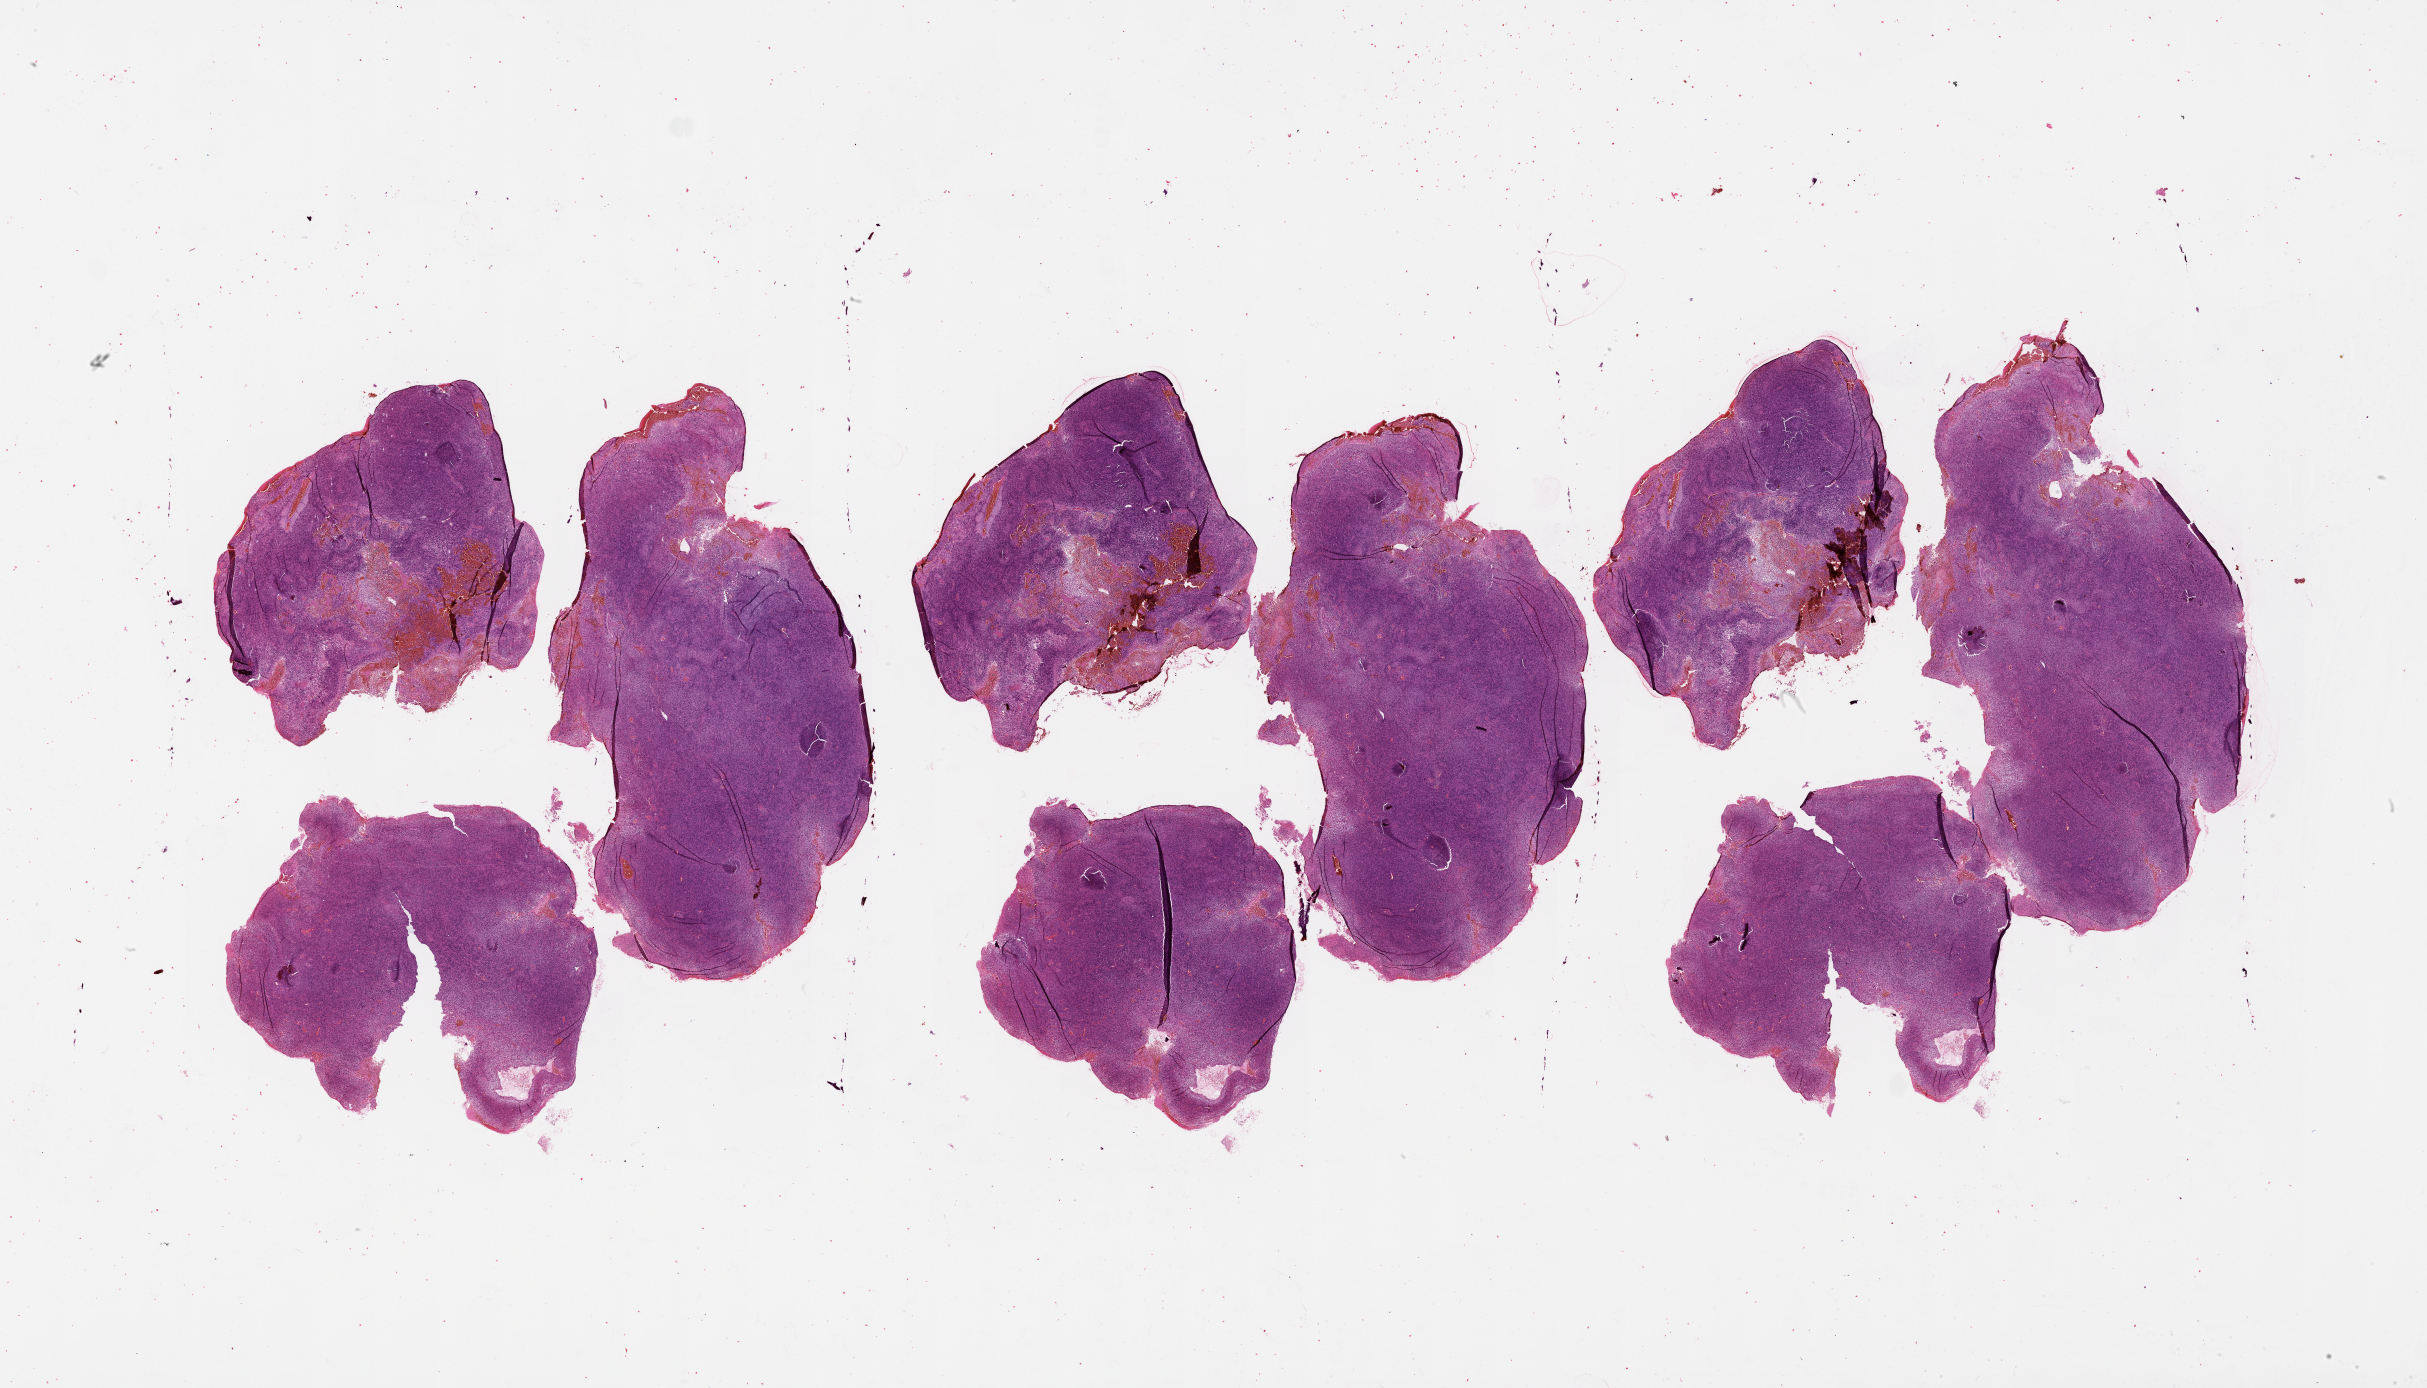
Hematoxylin and eosin (H&E) stained whole-slide image — whole scanned area (about 39.1 x 22.4 mm, from a 20x scan) shown as a low-resolution overview, brain, tumour tissue. Patient: female, age 37 years.
Histologic diagnosis: Glioblastoma. Primary tumour site (as recorded): occipital lobe.